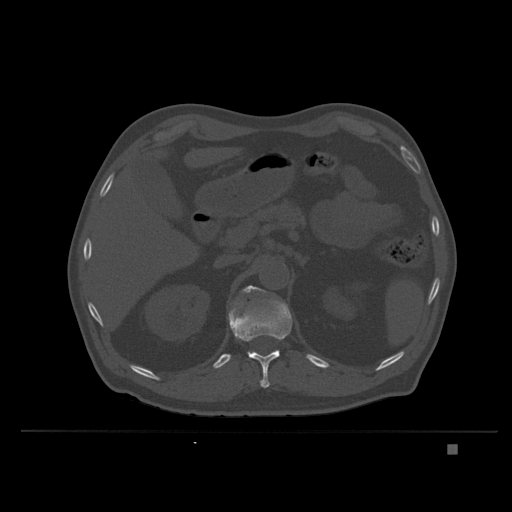
CT including the spine, one axial slice. Slice 155 of 435 in the series (ordered by position). Bone window (W 1800 / L 400 HU). 1.5 mm slice thickness. 512 × 512 image matrix, field of view 434 × 434 mm. Patient: male, 73 years. Case-level facts recorded for this patient, not image findings: primary cancer: skin.
Structures marked on this image (semi-automatic segmentation, software-assisted and operator-edited):
- T12 vertebra: bounding box <228,300,292,388> (left, top, right, bottom; pixels)